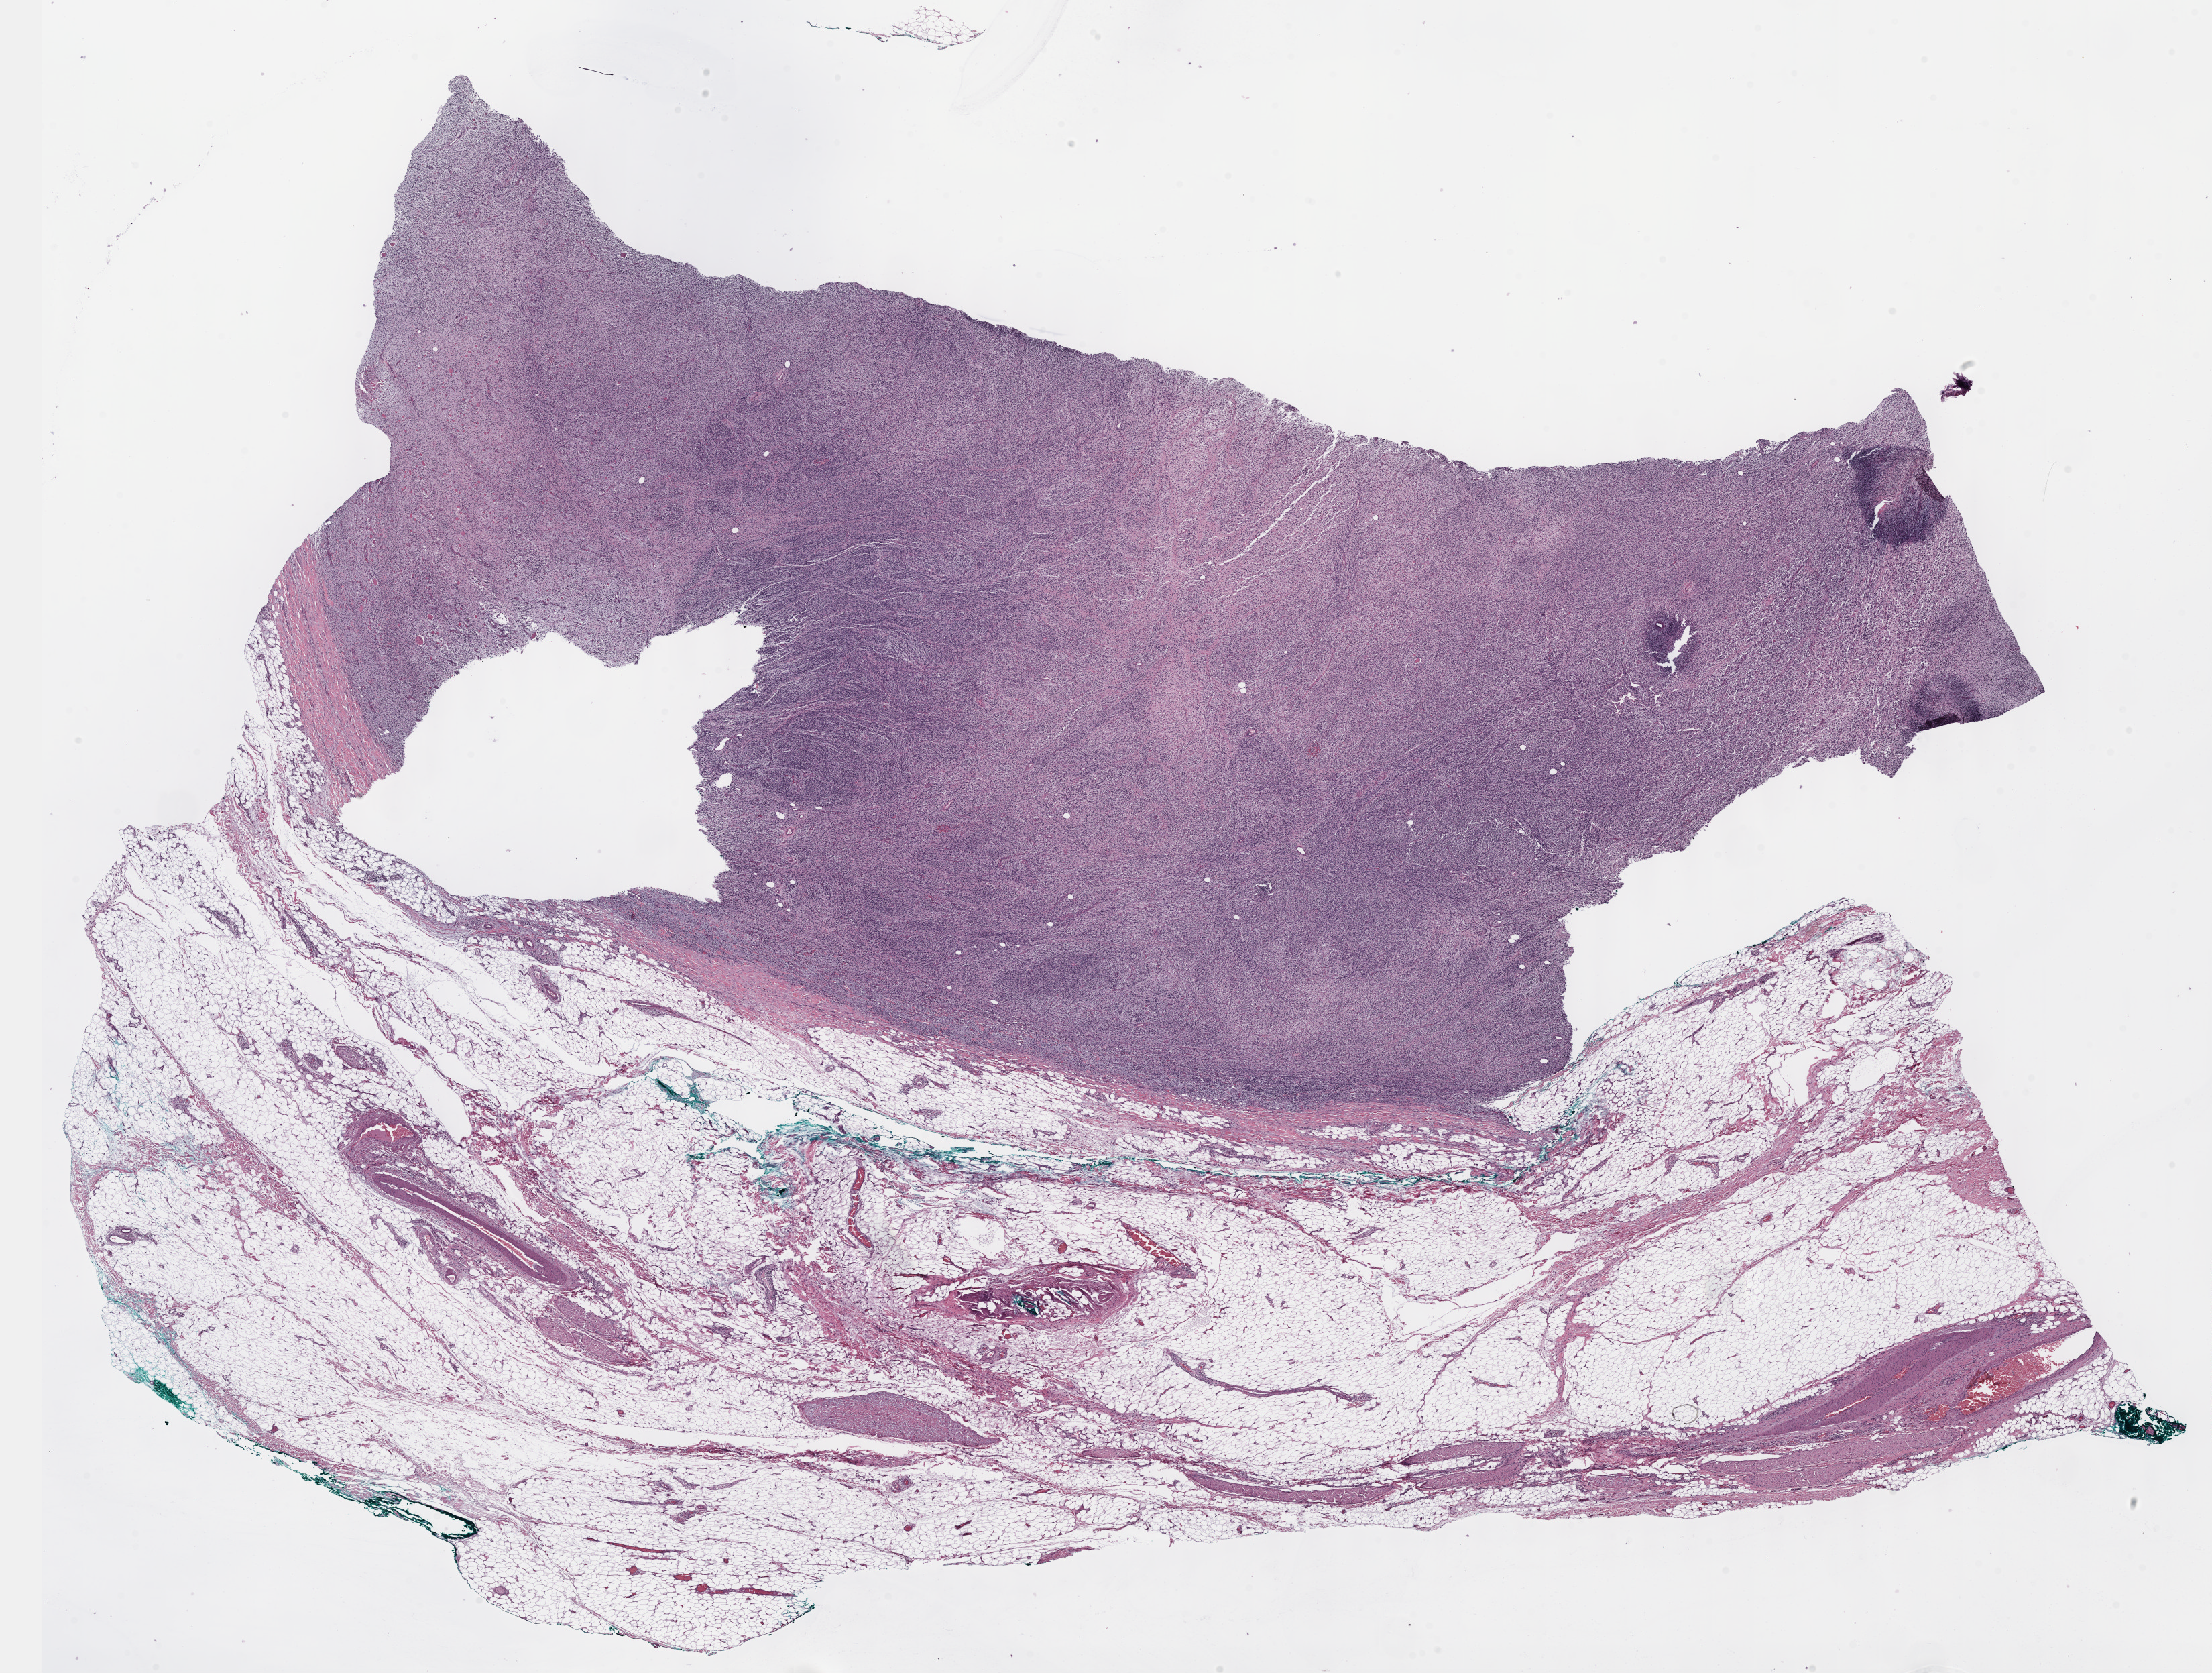
Whole-slide histology image, Hematoxylin and eosin (H&E) stained, shown as a low-resolution overview of the whole scanned area (about 26.7 x 20.2 mm), FFPE section, primary tumour sample from the connective, subcutaneous and other soft tissues. Female patient; age at initial diagnosis 34 years.
* diagnosis: Malignant peripheral nerve sheath tumor (connective, subcutaneous and other soft tissues of thorax)